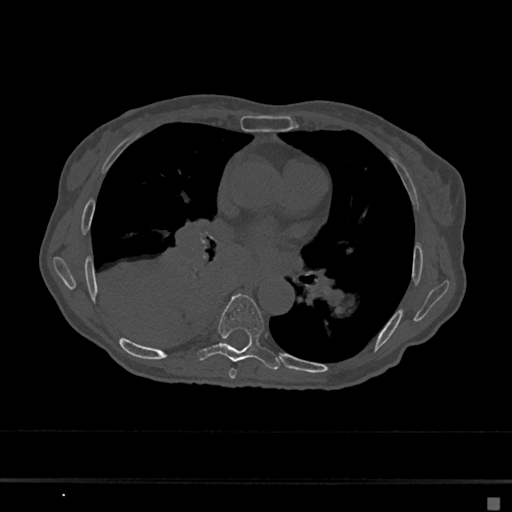
CT including the spine, one axial slice. Position 376 of 797 along the scan axis. Reconstruction kernel Br40s/3. Bone window (W 1800 / L 400 HU). 512 × 512 image matrix. Patient: female, 68 years. From the clinical record (not read from this slice): primary cancer: renal.
Outlined on this slice (semi-automatic segmentation, software-assisted and operator-edited):
- T6 vertebra: box from (x=228, y=368) to (x=237, y=379) px
- T7 vertebra: (x=197, y=294)–(x=280, y=370)